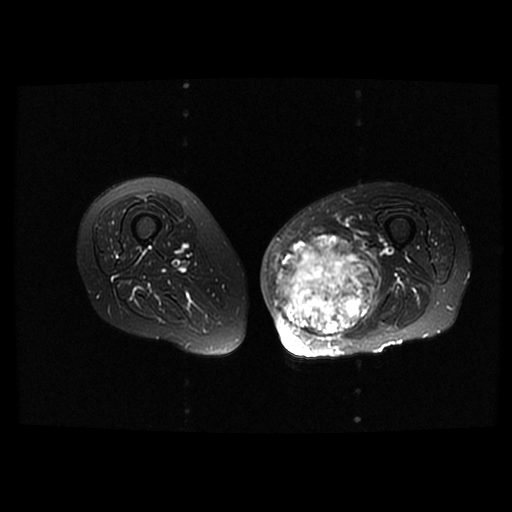
MRI of an extremity soft-tissue mass, one axial slice. Position 32 of 42 along the scan axis. T2-weighted fat-saturated. 6 mm slice thickness. 512 × 512 image matrix. Female patient. Case-level facts recorded for this patient, not image findings: histological type: pleomorphic leiomyosarcoma; grade: high; site of the primary tumour: left thigh.
Outlined on this slice (expert manual segmentation):
- gross tumour volume including surrounding oedema: bounding box <273,233,384,340> (left, top, right, bottom; pixels)
- gross tumour volume (mass): <273,233,378,338>